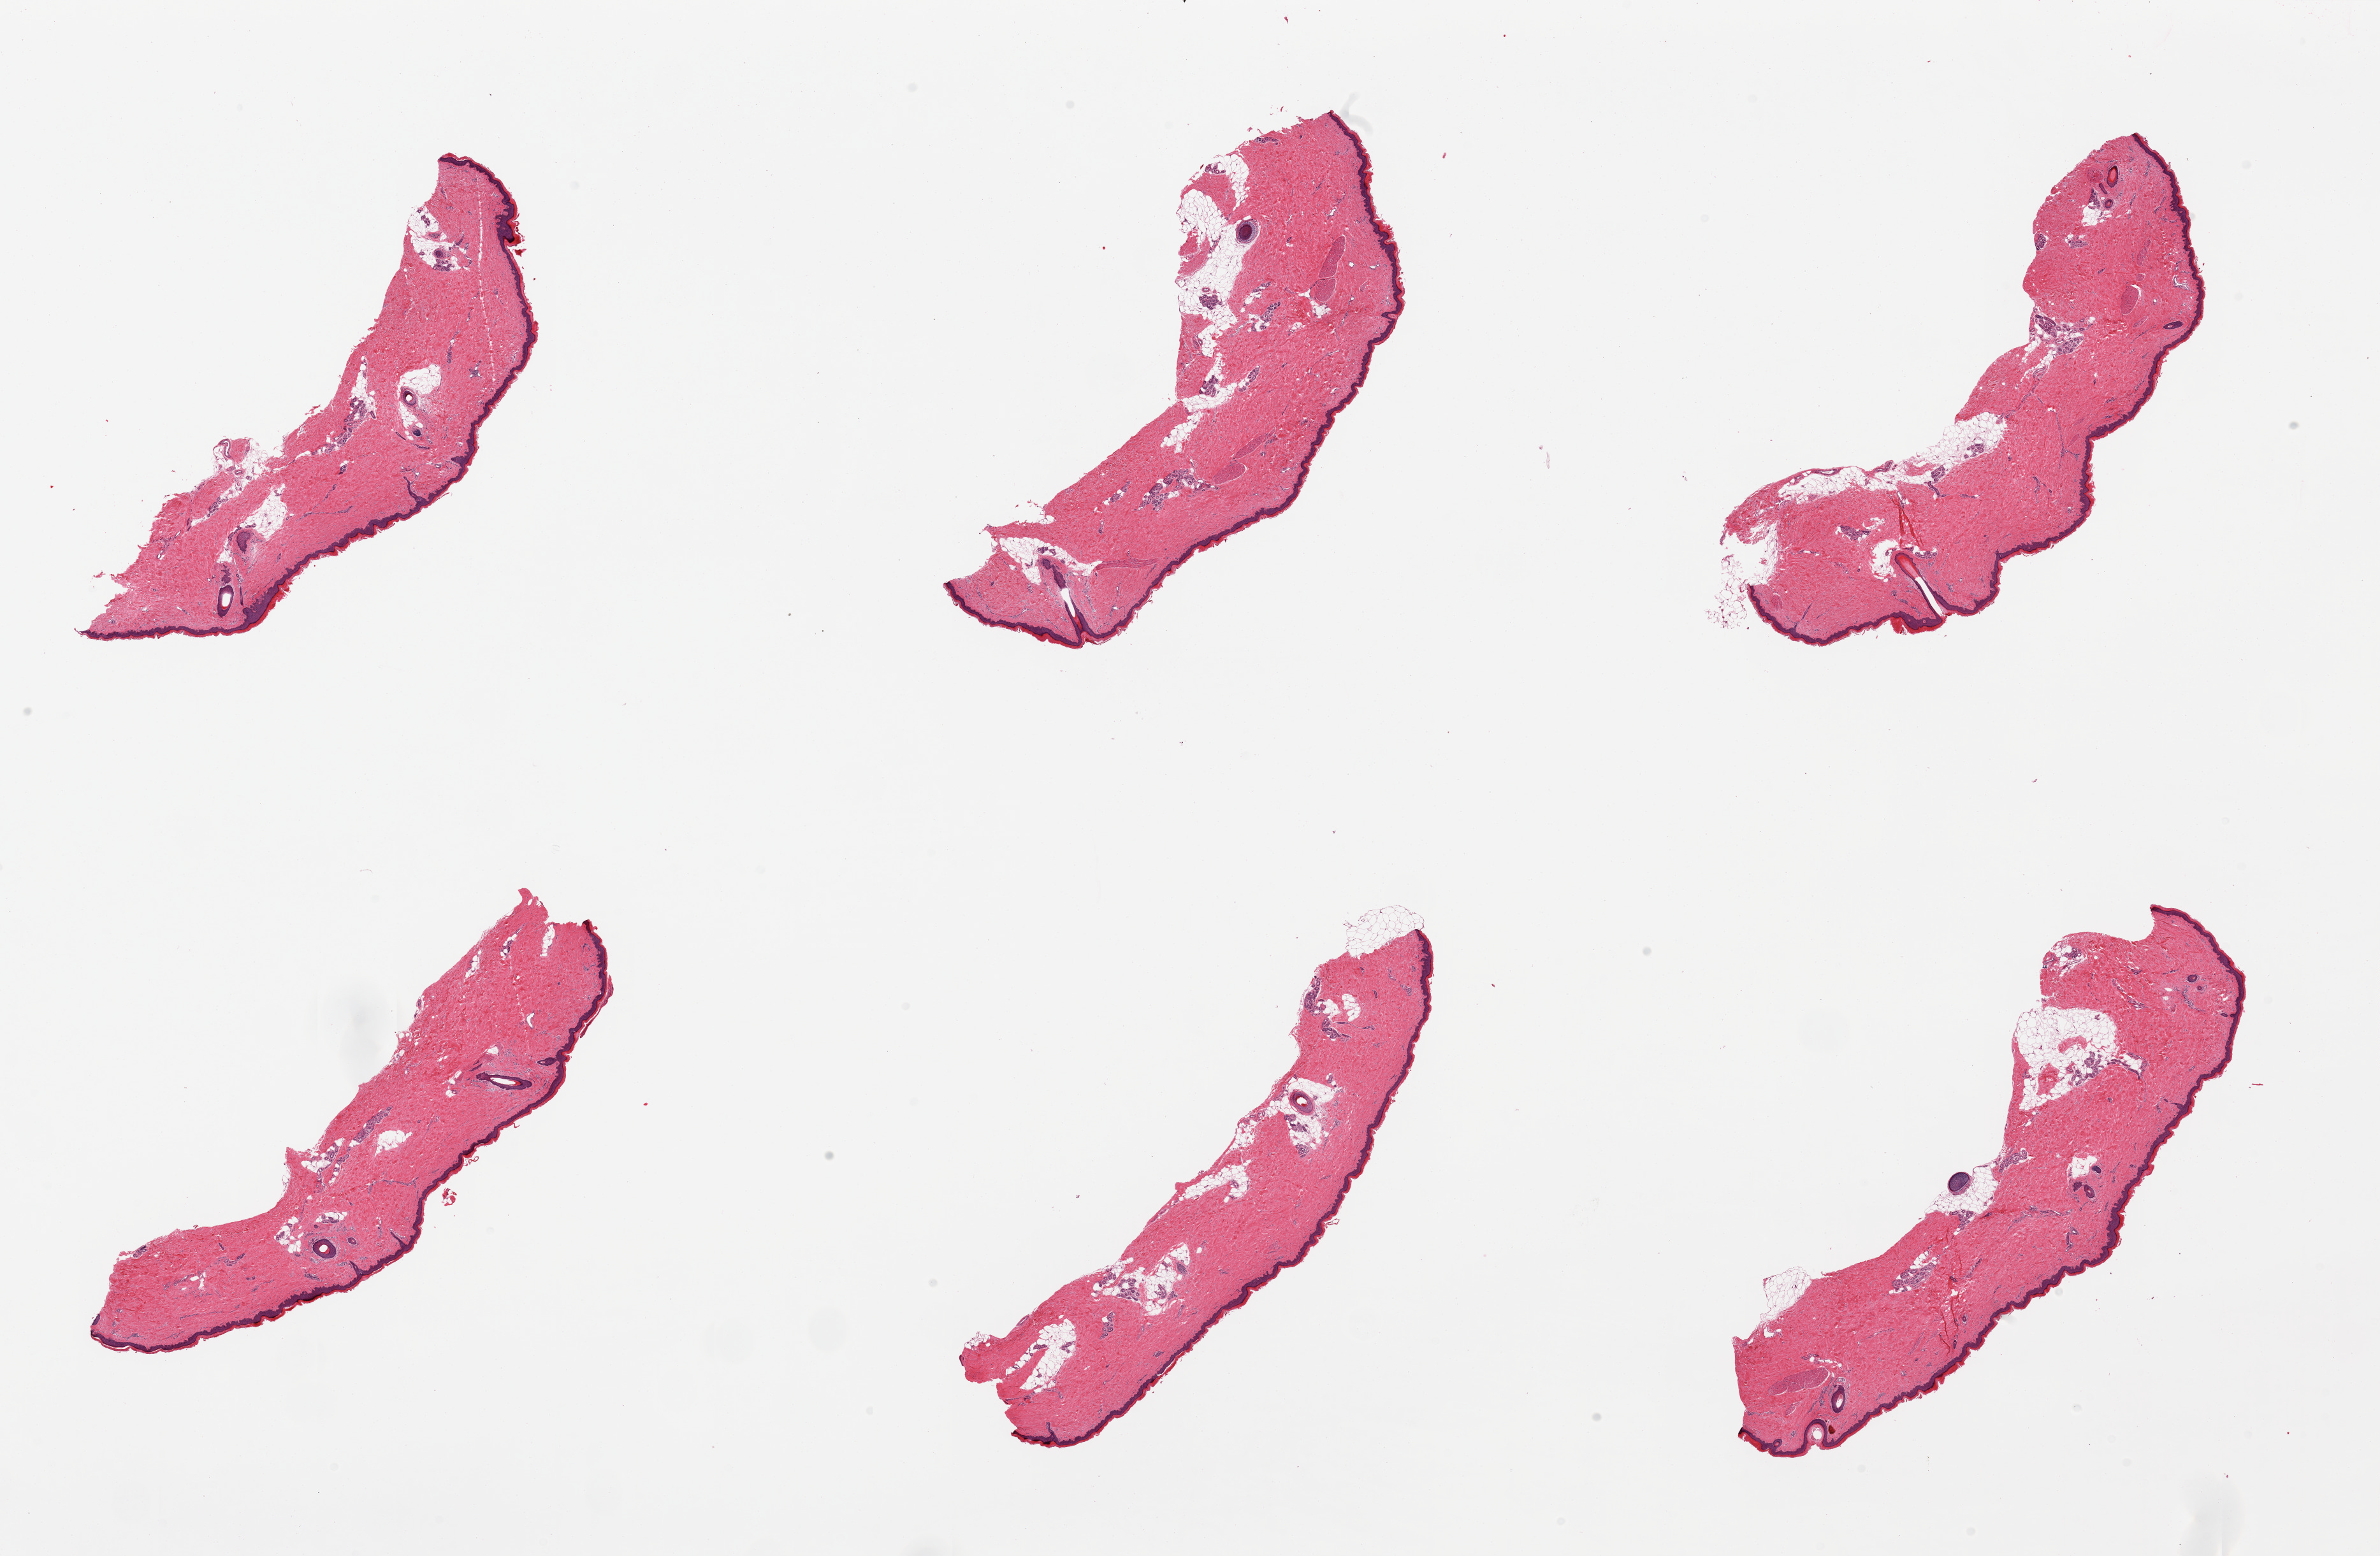
Haematoxylin and eosin whole-slide image, a low-resolution overview of the entire scanned area, about 29.5 x 19.3 mm (from a 20x scan); PAXgene-fixed, paraffin-embedded tissue; sampled site (target tissue): skin of lower leg; donor tissue sample. Donor sex: female.
Reviewer comment on this tissue sample: 6 pieces, minimal dermal fat, squamous epitheliums is ~50-60 microns, <!% thickness.